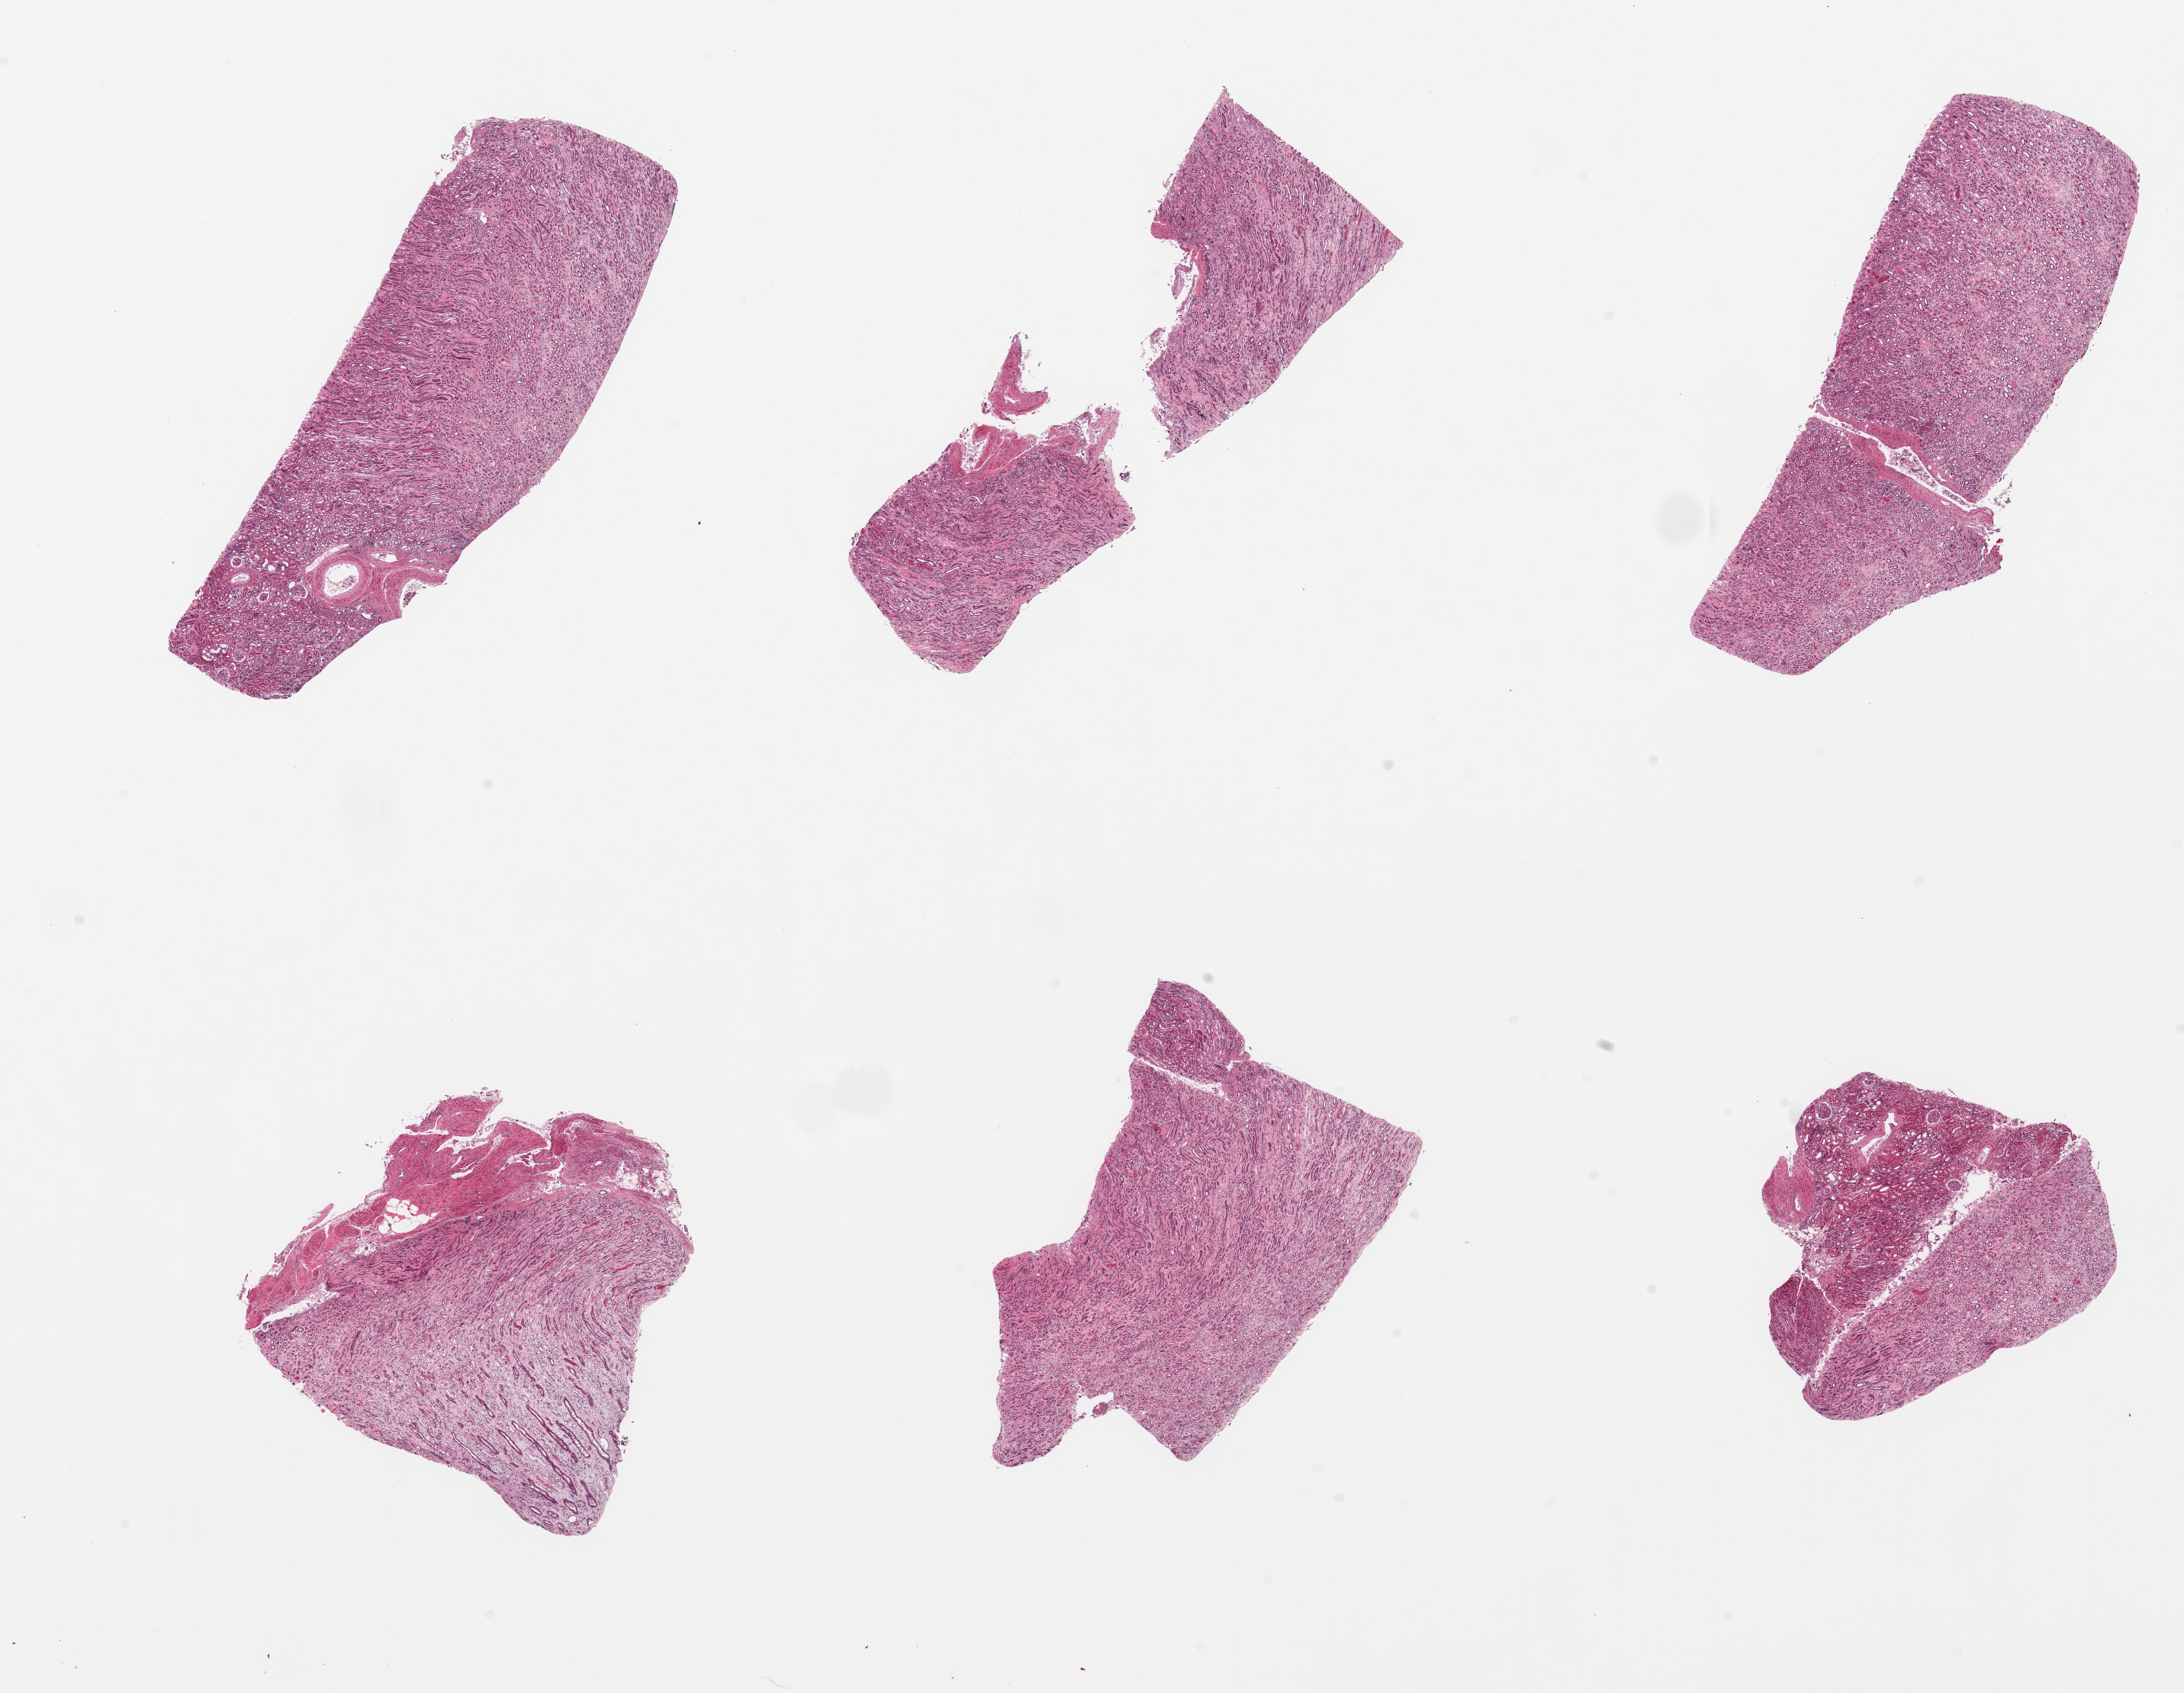
Haematoxylin and eosin whole-slide image, brightfield, whole scanned area (about 22.6 x 17.5 mm) shown as a low-resolution overview, PAXgene-fixed, paraffin-embedded tissue, section of renal cortex (target tissue), donor tissue sample. Male donor.
Review note (as recorded): 6 pieces, 90% medulla, trace cortex--not sufficient glomeruli to qualify as target cortex.